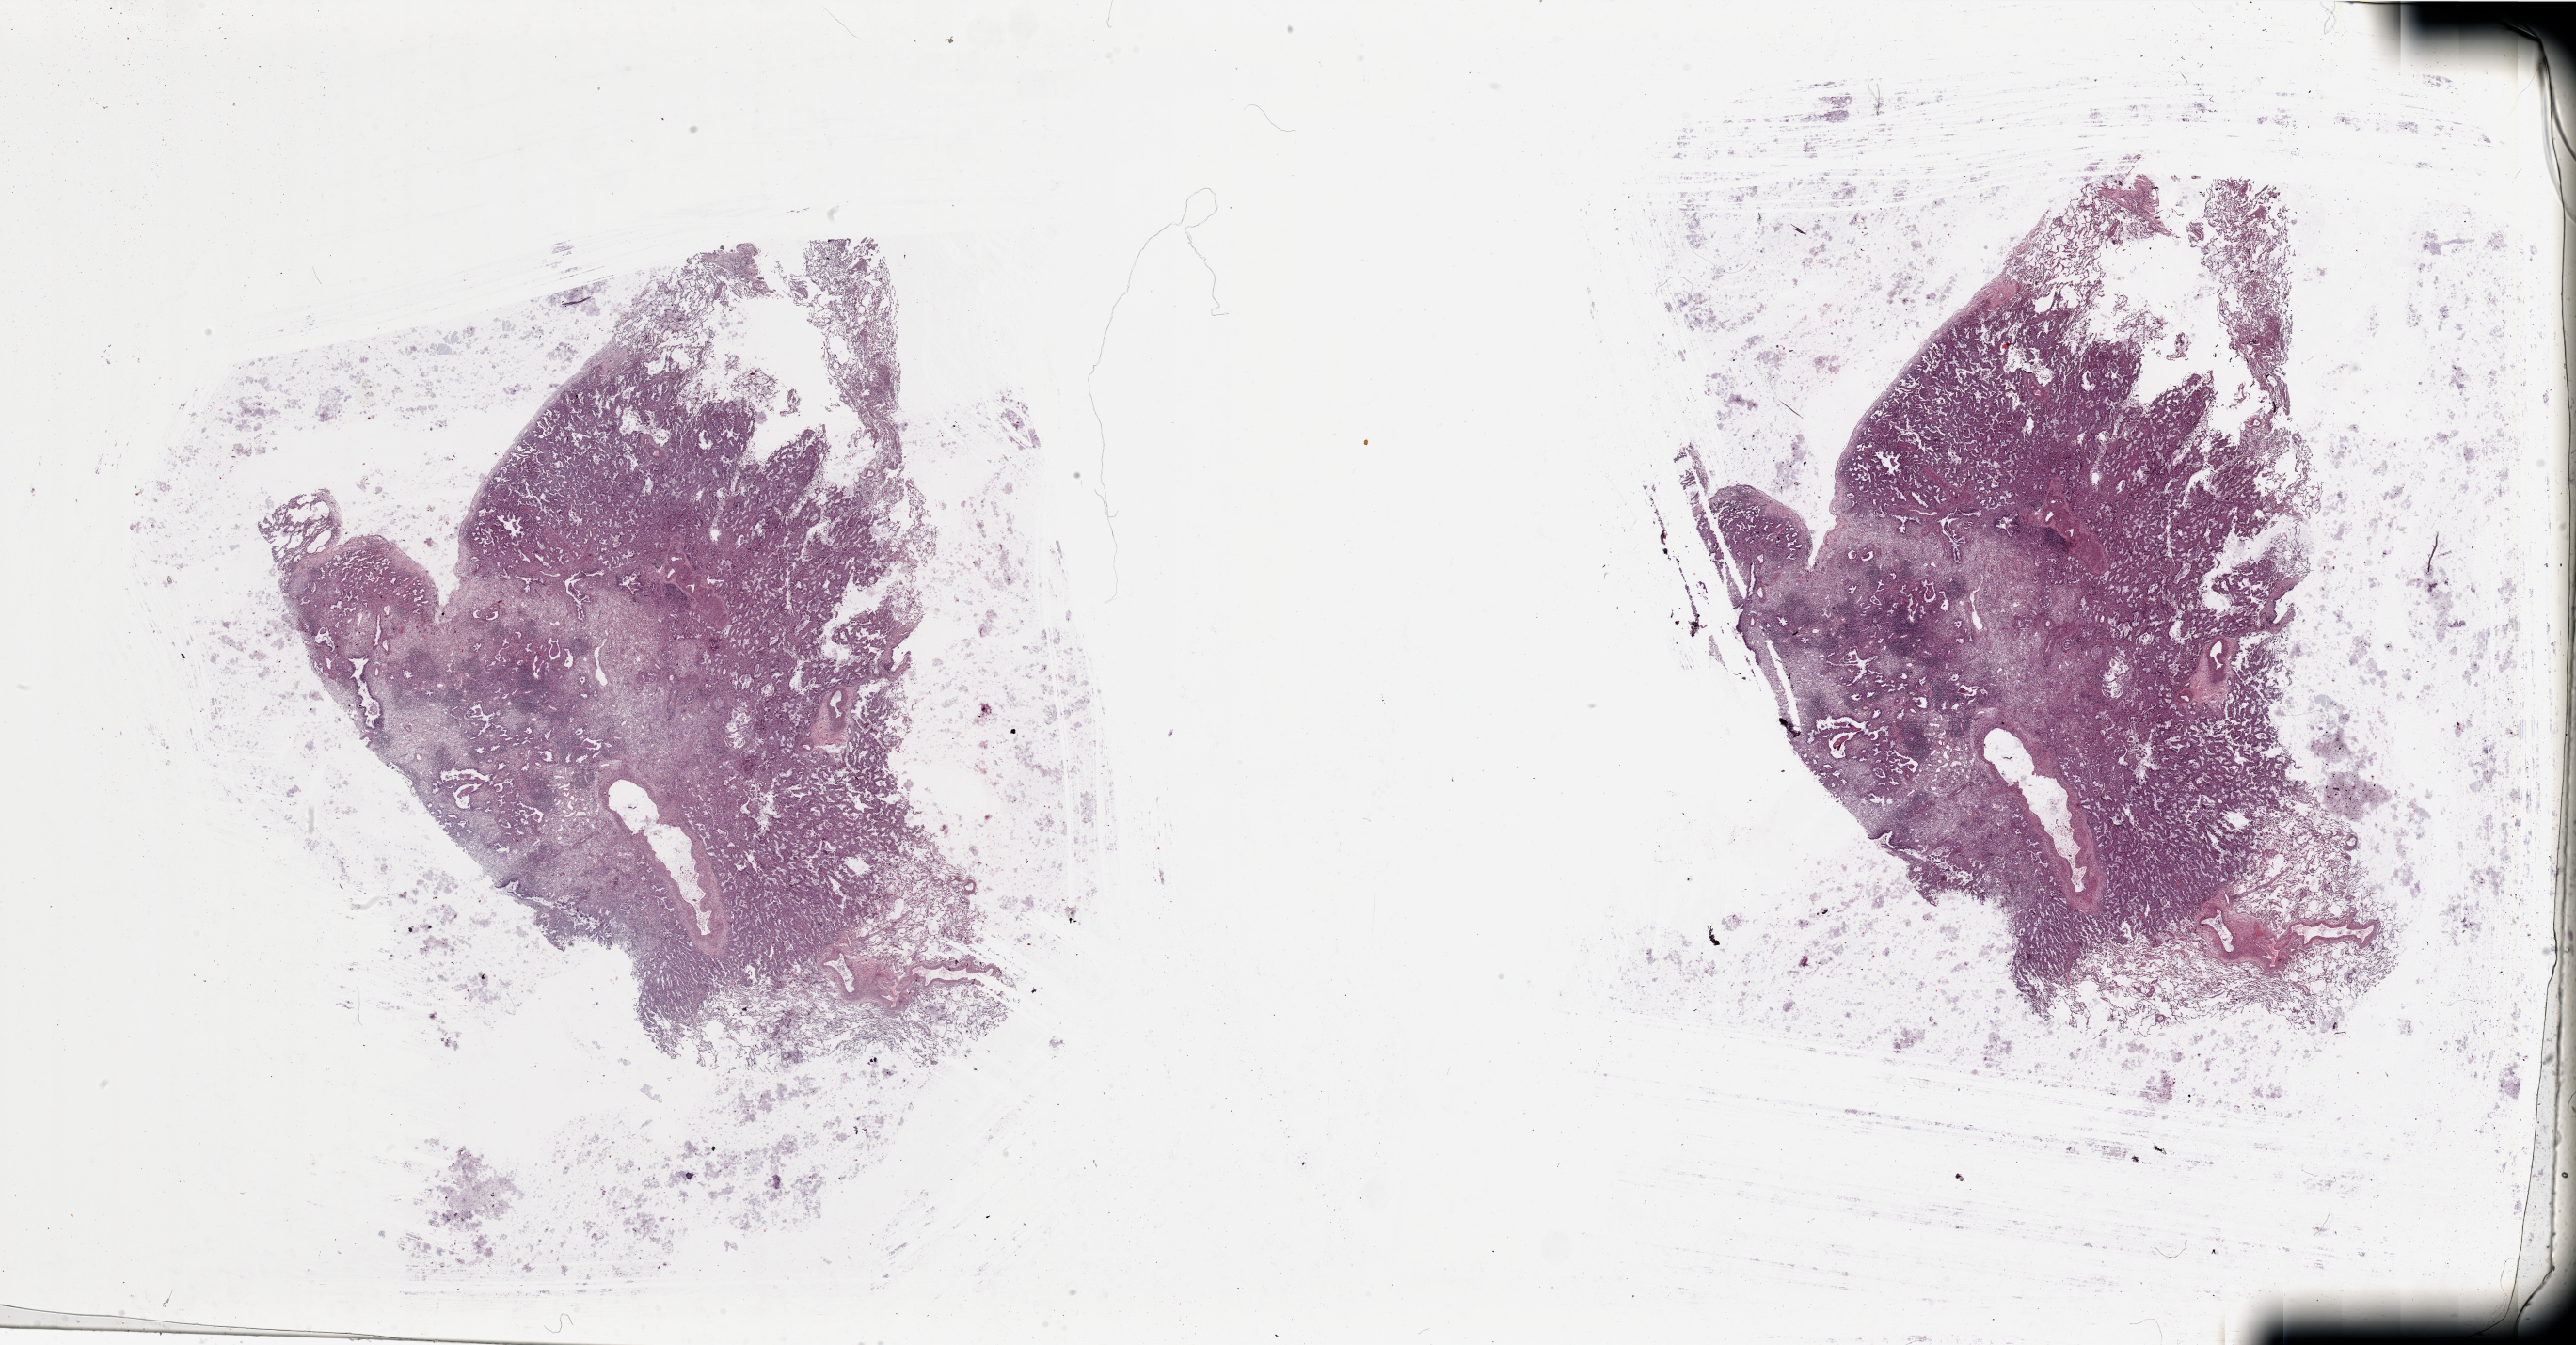
H&E whole-slide image — low-resolution overview of the scanned area, about 43.3 x 22.6 mm. Tumour tissue sample, sampled site: lung. Female, 61 y/o. Histologic grade: G1 (well differentiated). Pathologist review of this section (percent, as recorded): tumour nuclei 65%, necrosis 7%.
• AJCC pathologic stage: IA
• primary tumour site (as recorded): right lower lobe
• diagnosis: Adenocarcinoma, NOS